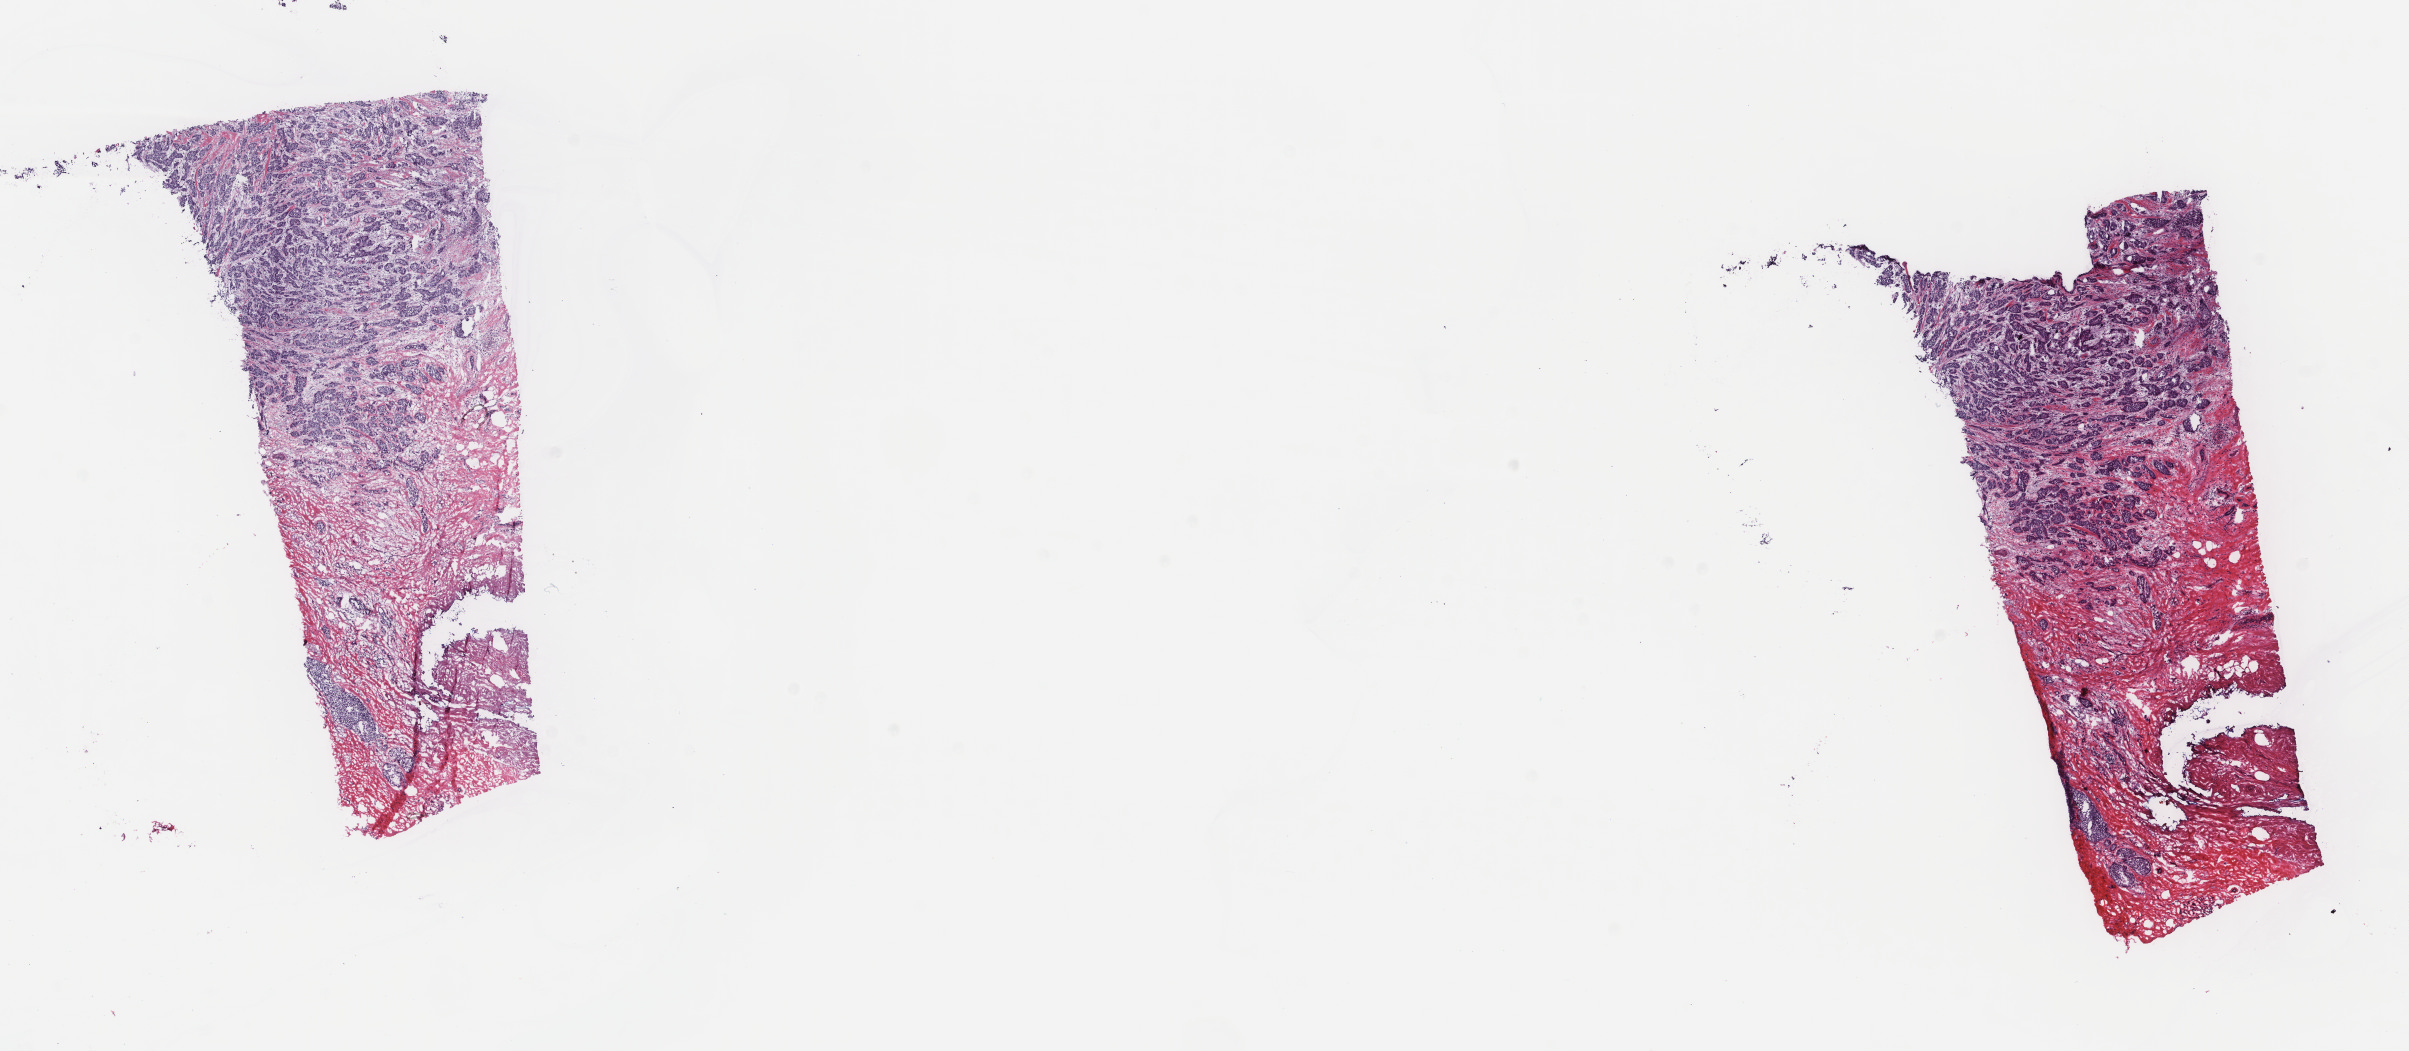
Digitized H&E tissue section (whole slide), whole scanned area (about 19.1 x 8.3 mm, from a 40x scan) shown as a low-resolution overview, frozen section from the top of the tissue portion, breast, primary tumour sample. Female, age 70 years at initial diagnosis. Slide review estimates, as recorded: tumour cells 65%, tumour nuclei 85%, normal cells 1%, stromal cells 34%, necrosis 0%. Infiltration values recorded for this section: lymphocyte infiltration 1%, monocyte infiltration 0%, neutrophil infiltration 0%.
* AJCC pathologic stage: I (6th edition)
* histologic diagnosis: Infiltrating duct carcinoma, NOS
* lymph nodes positive (case pathology): 0 of 2 examined